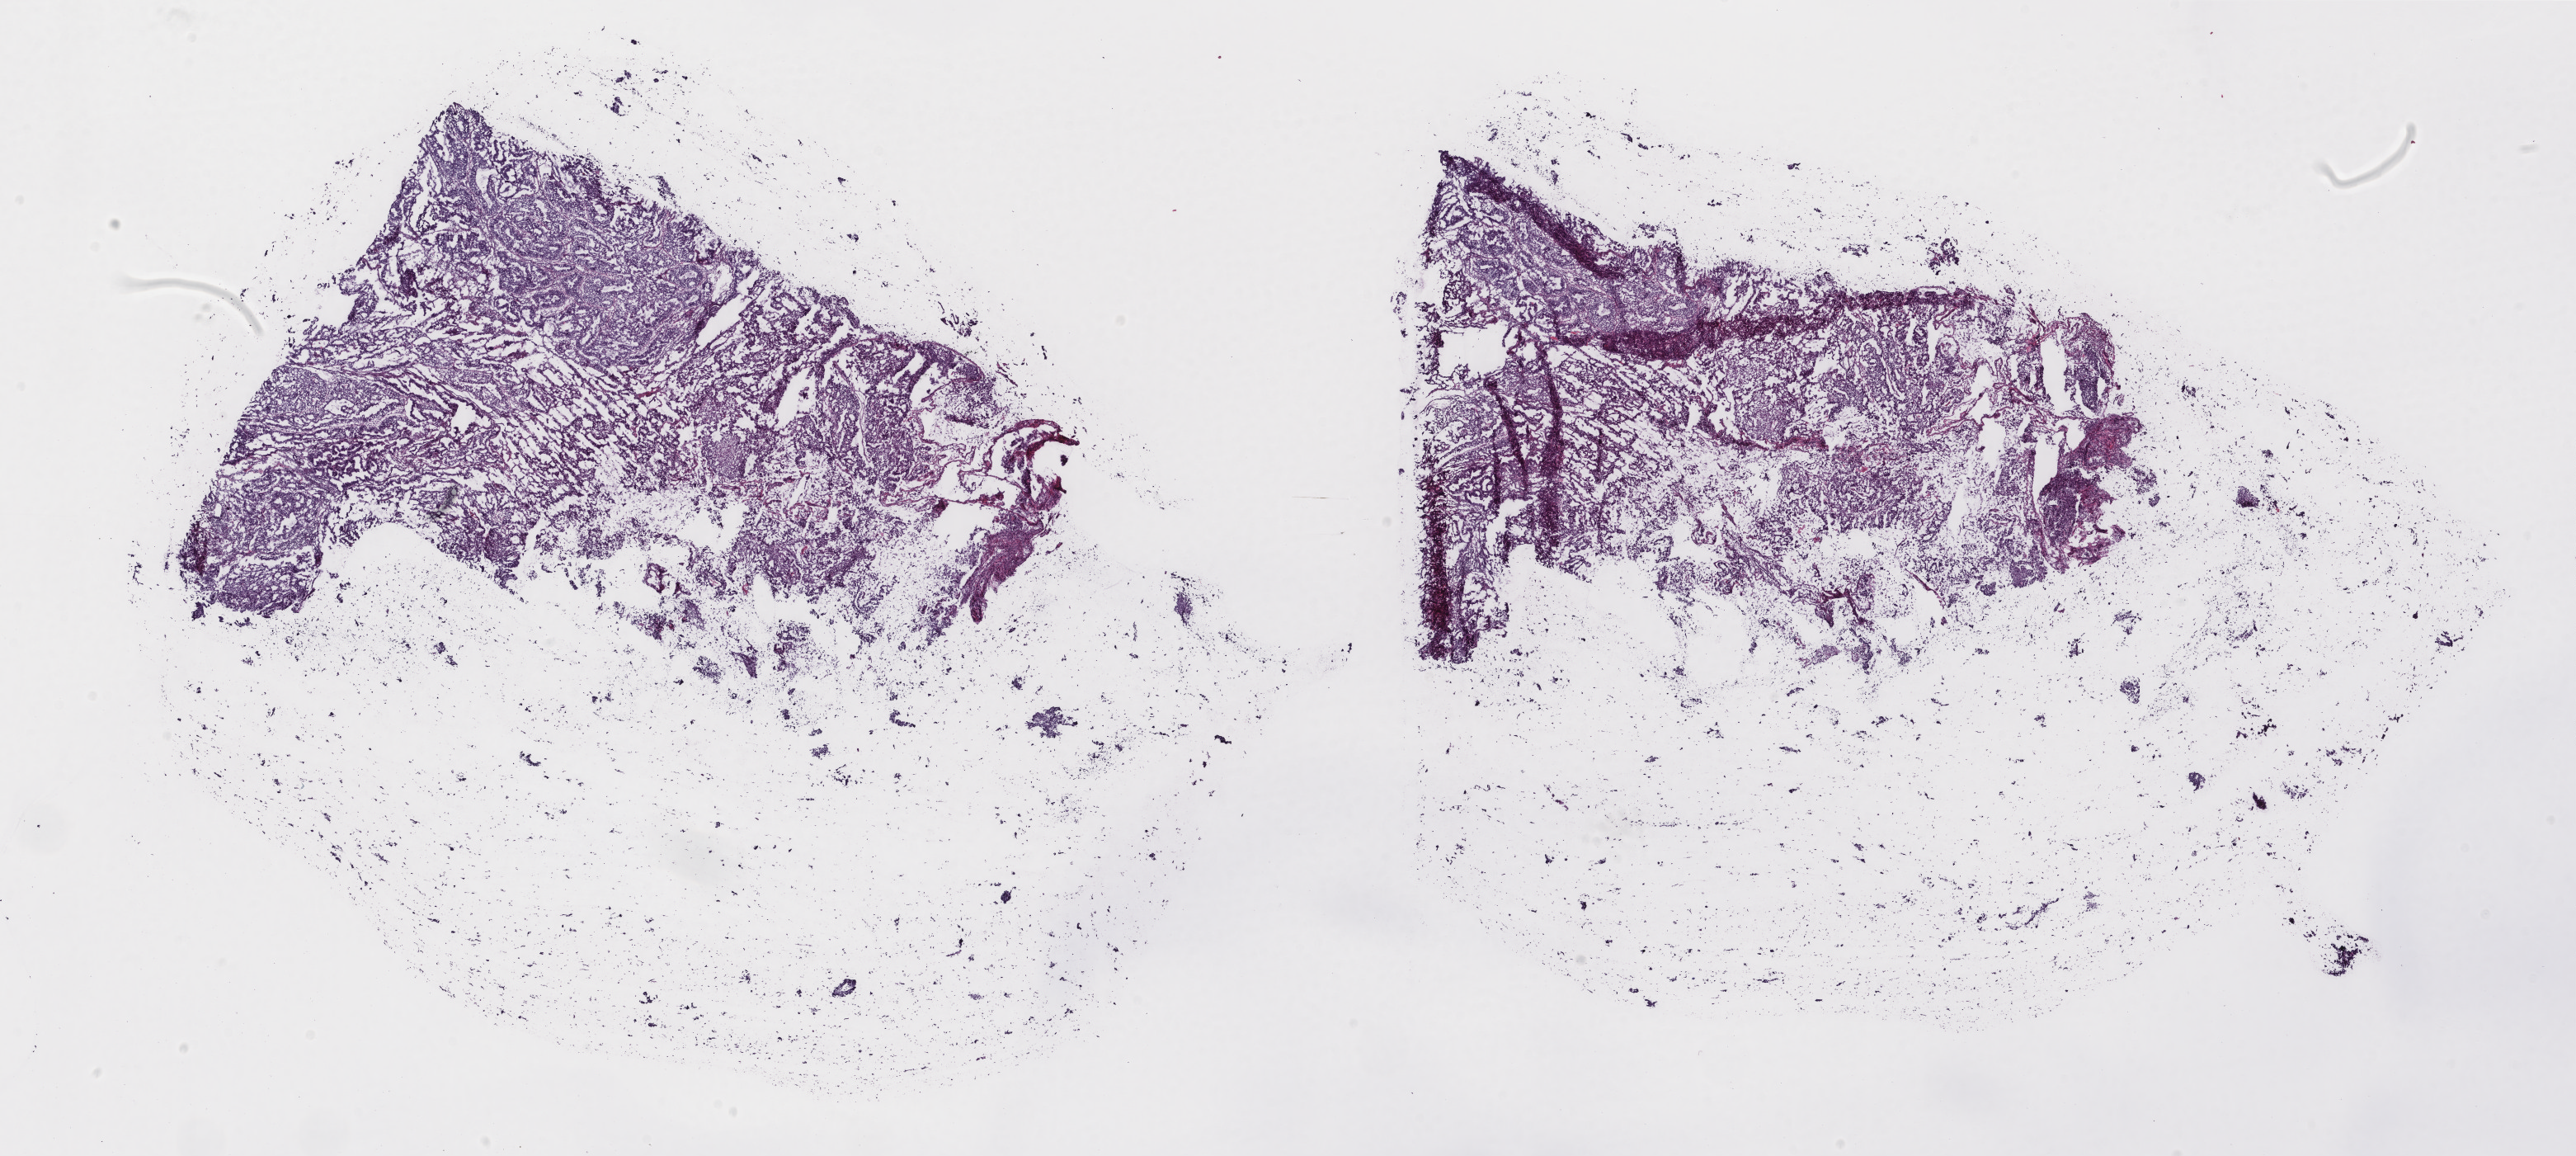
Digitized H&E-stained tissue section (whole slide), low-resolution overview of the scanned area, about 24.8 x 11.1 mm, frozen section from the top of the tissue portion, uterus, primary tumour sample. Patient: female, age at initial diagnosis 72 years. Histologic grade: G2 (moderately differentiated). Pathologist review of this section (percent, as recorded): tumour cells 60%, tumour nuclei 60%, normal cells 0%, stromal cells 30%, necrosis 10%. Infiltration values recorded for this section: lymphocyte infiltration 40%, monocyte infiltration 20%, neutrophil infiltration 20%.
Histologic diagnosis: Endometrioid adenocarcinoma, NOS (endometrium). FIGO stage: IA.